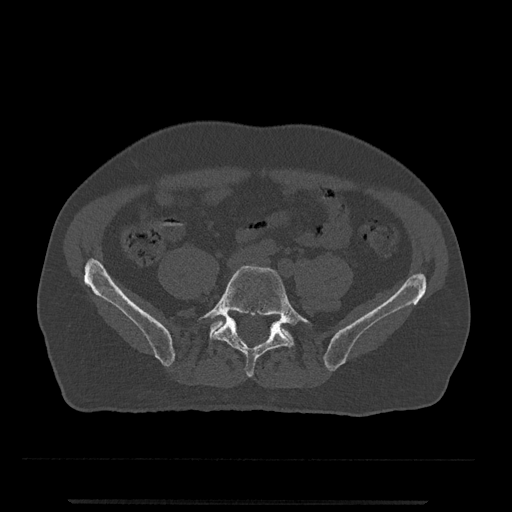
CT including the spine, one axial slice. Slice 69 of 797 in the series (ordered by position). Reconstruction kernel Br40s/3. Bone window (W 1800 / L 400 HU). 0.5 mm slice thickness. 512 × 512 image matrix. Patient: male, 63 years. Case-level facts recorded for this patient, not image findings: primary cancer: prostate.
Structures marked on this image (semi-automatic segmentation, software-assisted and operator-edited):
- L5 vertebra: box from (x=197, y=266) to (x=313, y=377) px